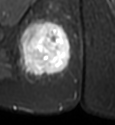
MRI of an extremity soft-tissue mass, one axial slice. Position 23 of 49 along the scan axis. STIR. MR volume resampled by the dataset authors to the PET/CT grid (not the native acquisition matrix). 3.27 mm slice thickness. 115 × 125 image matrix. Female patient. Case-level facts recorded for this patient, not image findings: histological type: epithelioid sarcoma; grade: intermediate; site of the primary tumour: right buttock.
Annotated regions visible in this slice (expert contour drawn on MRI and transferred to this co-registered scan by the dataset authors):
- gross tumour volume including surrounding oedema: bounding box [x1, y1, x2, y2] px = [17, 18, 71, 76]
- gross tumour volume (mass): [22, 21, 71, 74]